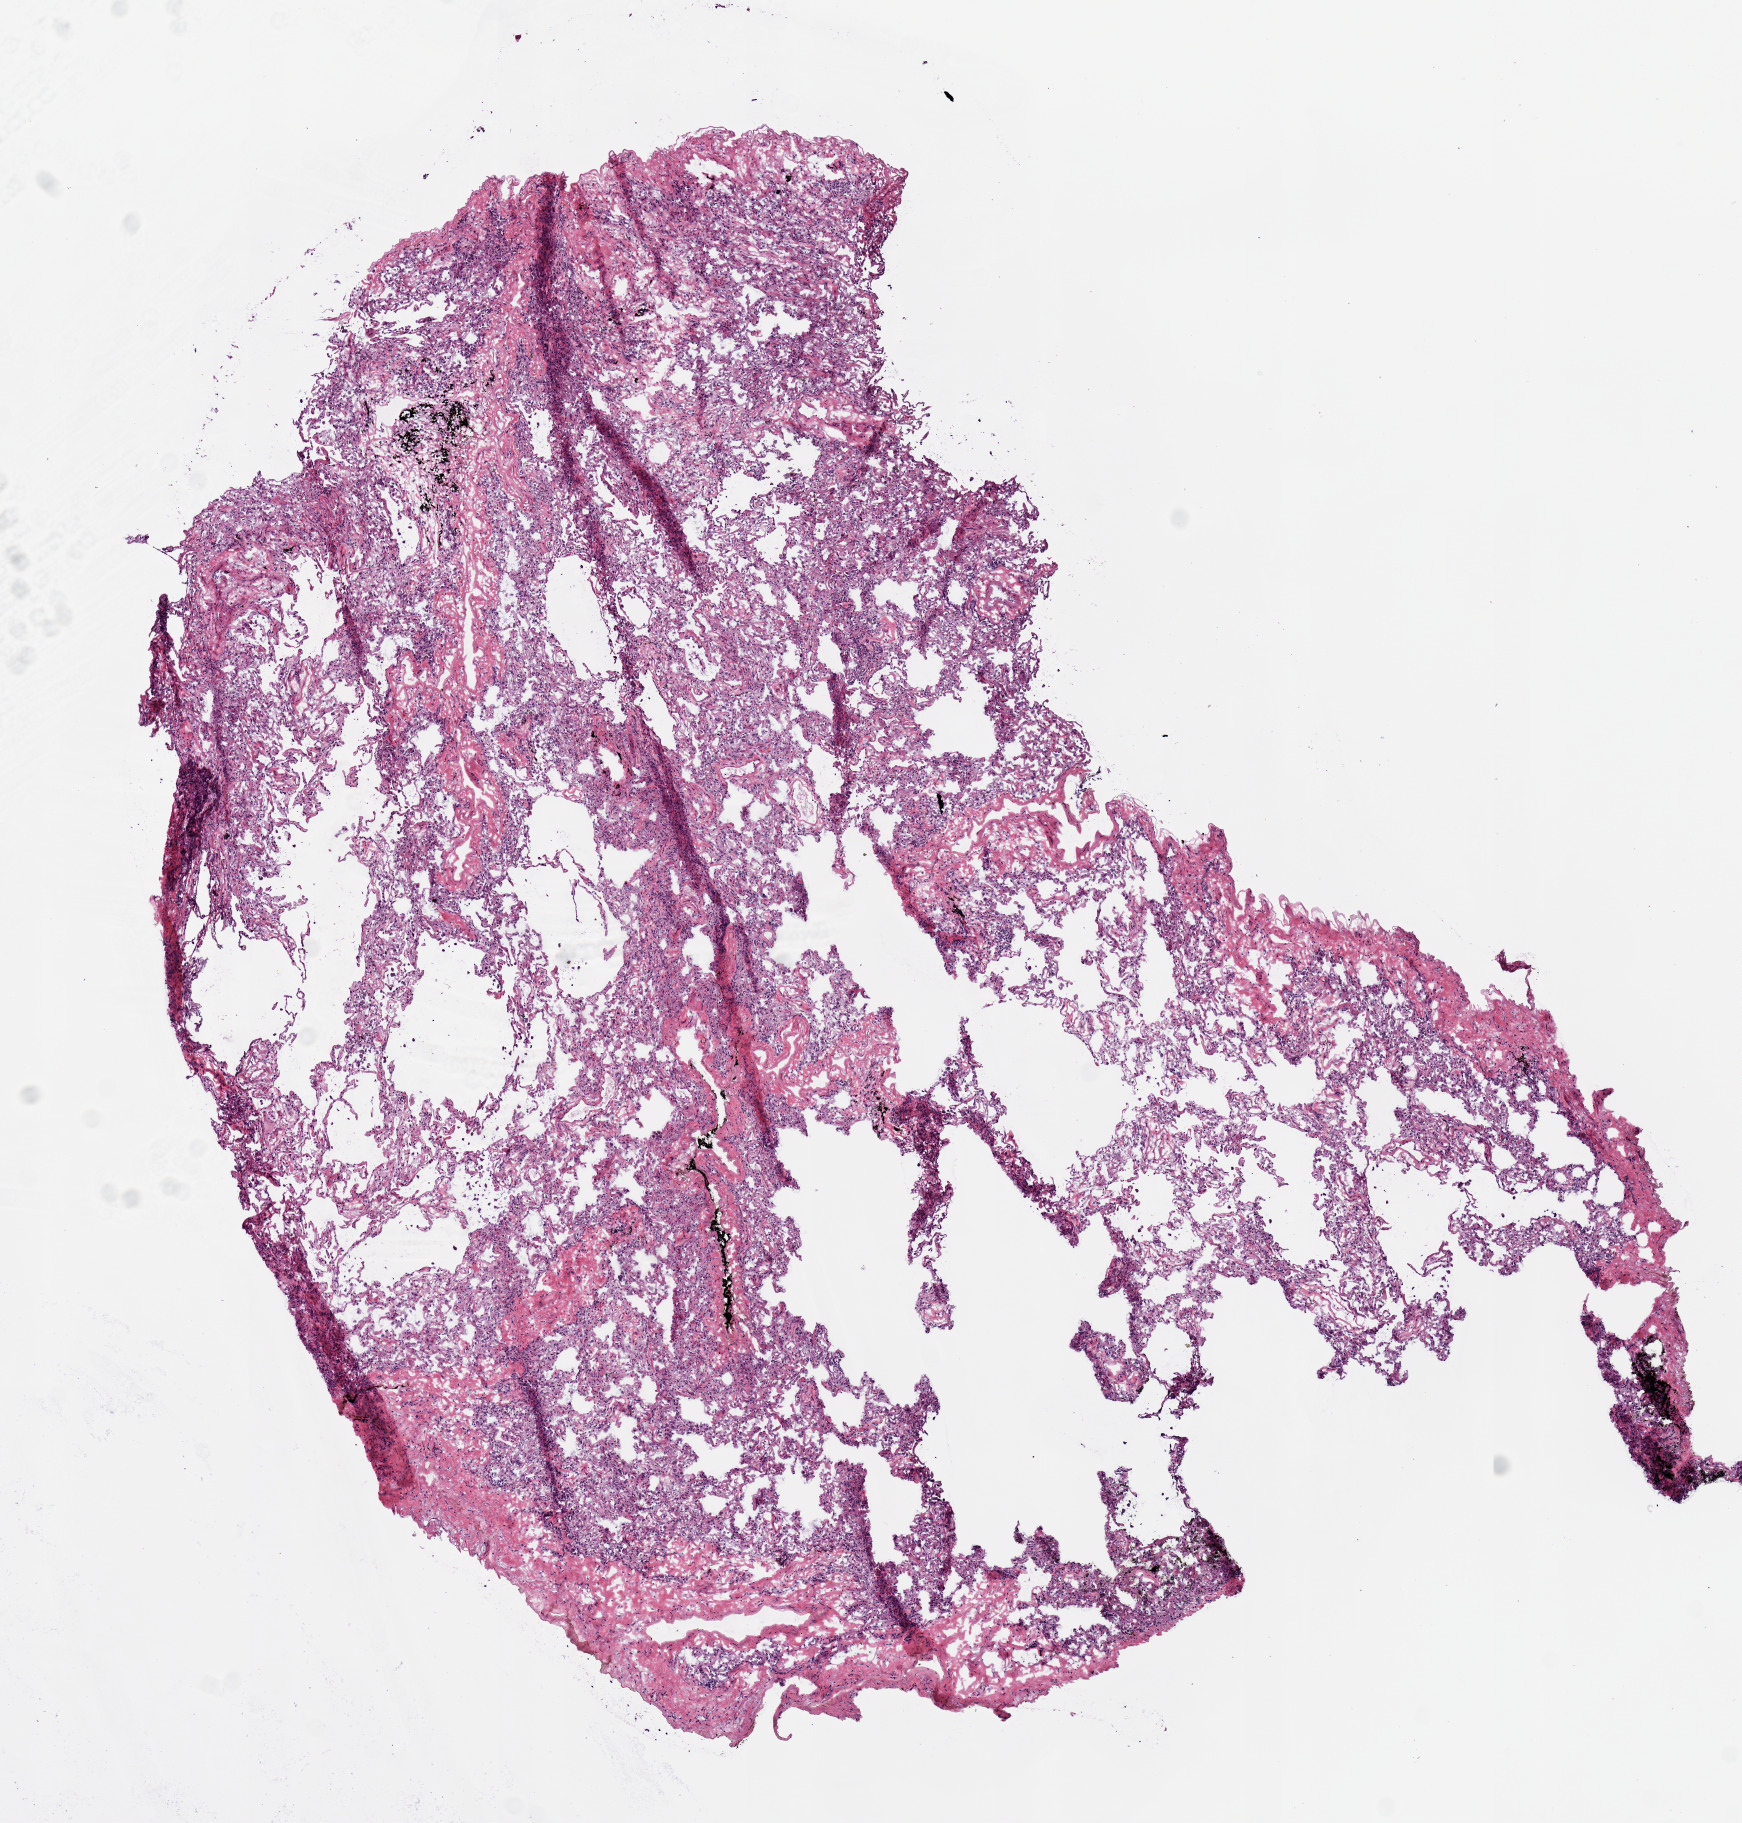
Whole-slide histology image, Hematoxylin and eosin (H&E) stained — low-resolution overview of the scanned area, about 6.9 x 7.2 mm. Frozen section from the top of the tissue portion. Lung, solid tissue normal (non-tumour tissue) sample. Female patient; age at initial diagnosis 71 years.
This section: solid tissue normal sample (biorepository sample class). Patient diagnosis: Adenocarcinoma, NOS (lower lobe, lung).